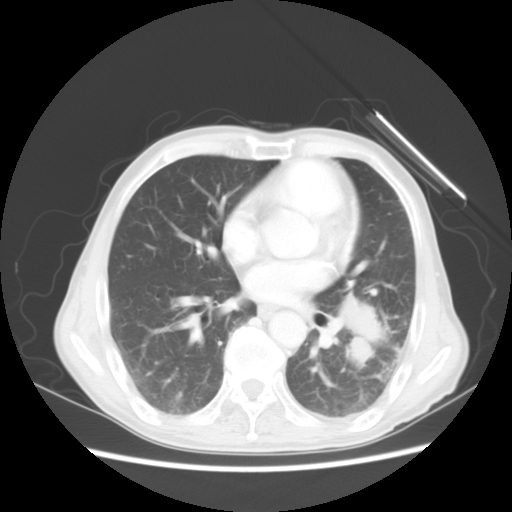
Chest CT, one axial slice; slice 23 of 51 in the series (ordered by position); reconstruction kernel STANDARD; lung window (W 1500 / L -600 HU); 5 mm slice thickness; 512 × 512 image matrix, field of view 360 × 360 mm. Male patient, age 64 years. Case-level facts recorded for this patient, not image findings: clinical TNM (as recorded): T4 N0 M0; histopathological grade: G2-3.
Annotated regions visible in this slice (bounding box drawn by a radiologist):
- lung tumour (recorded histology: squamous cell carcinoma): bounding box <332,280,387,370> (left, top, right, bottom; pixels)